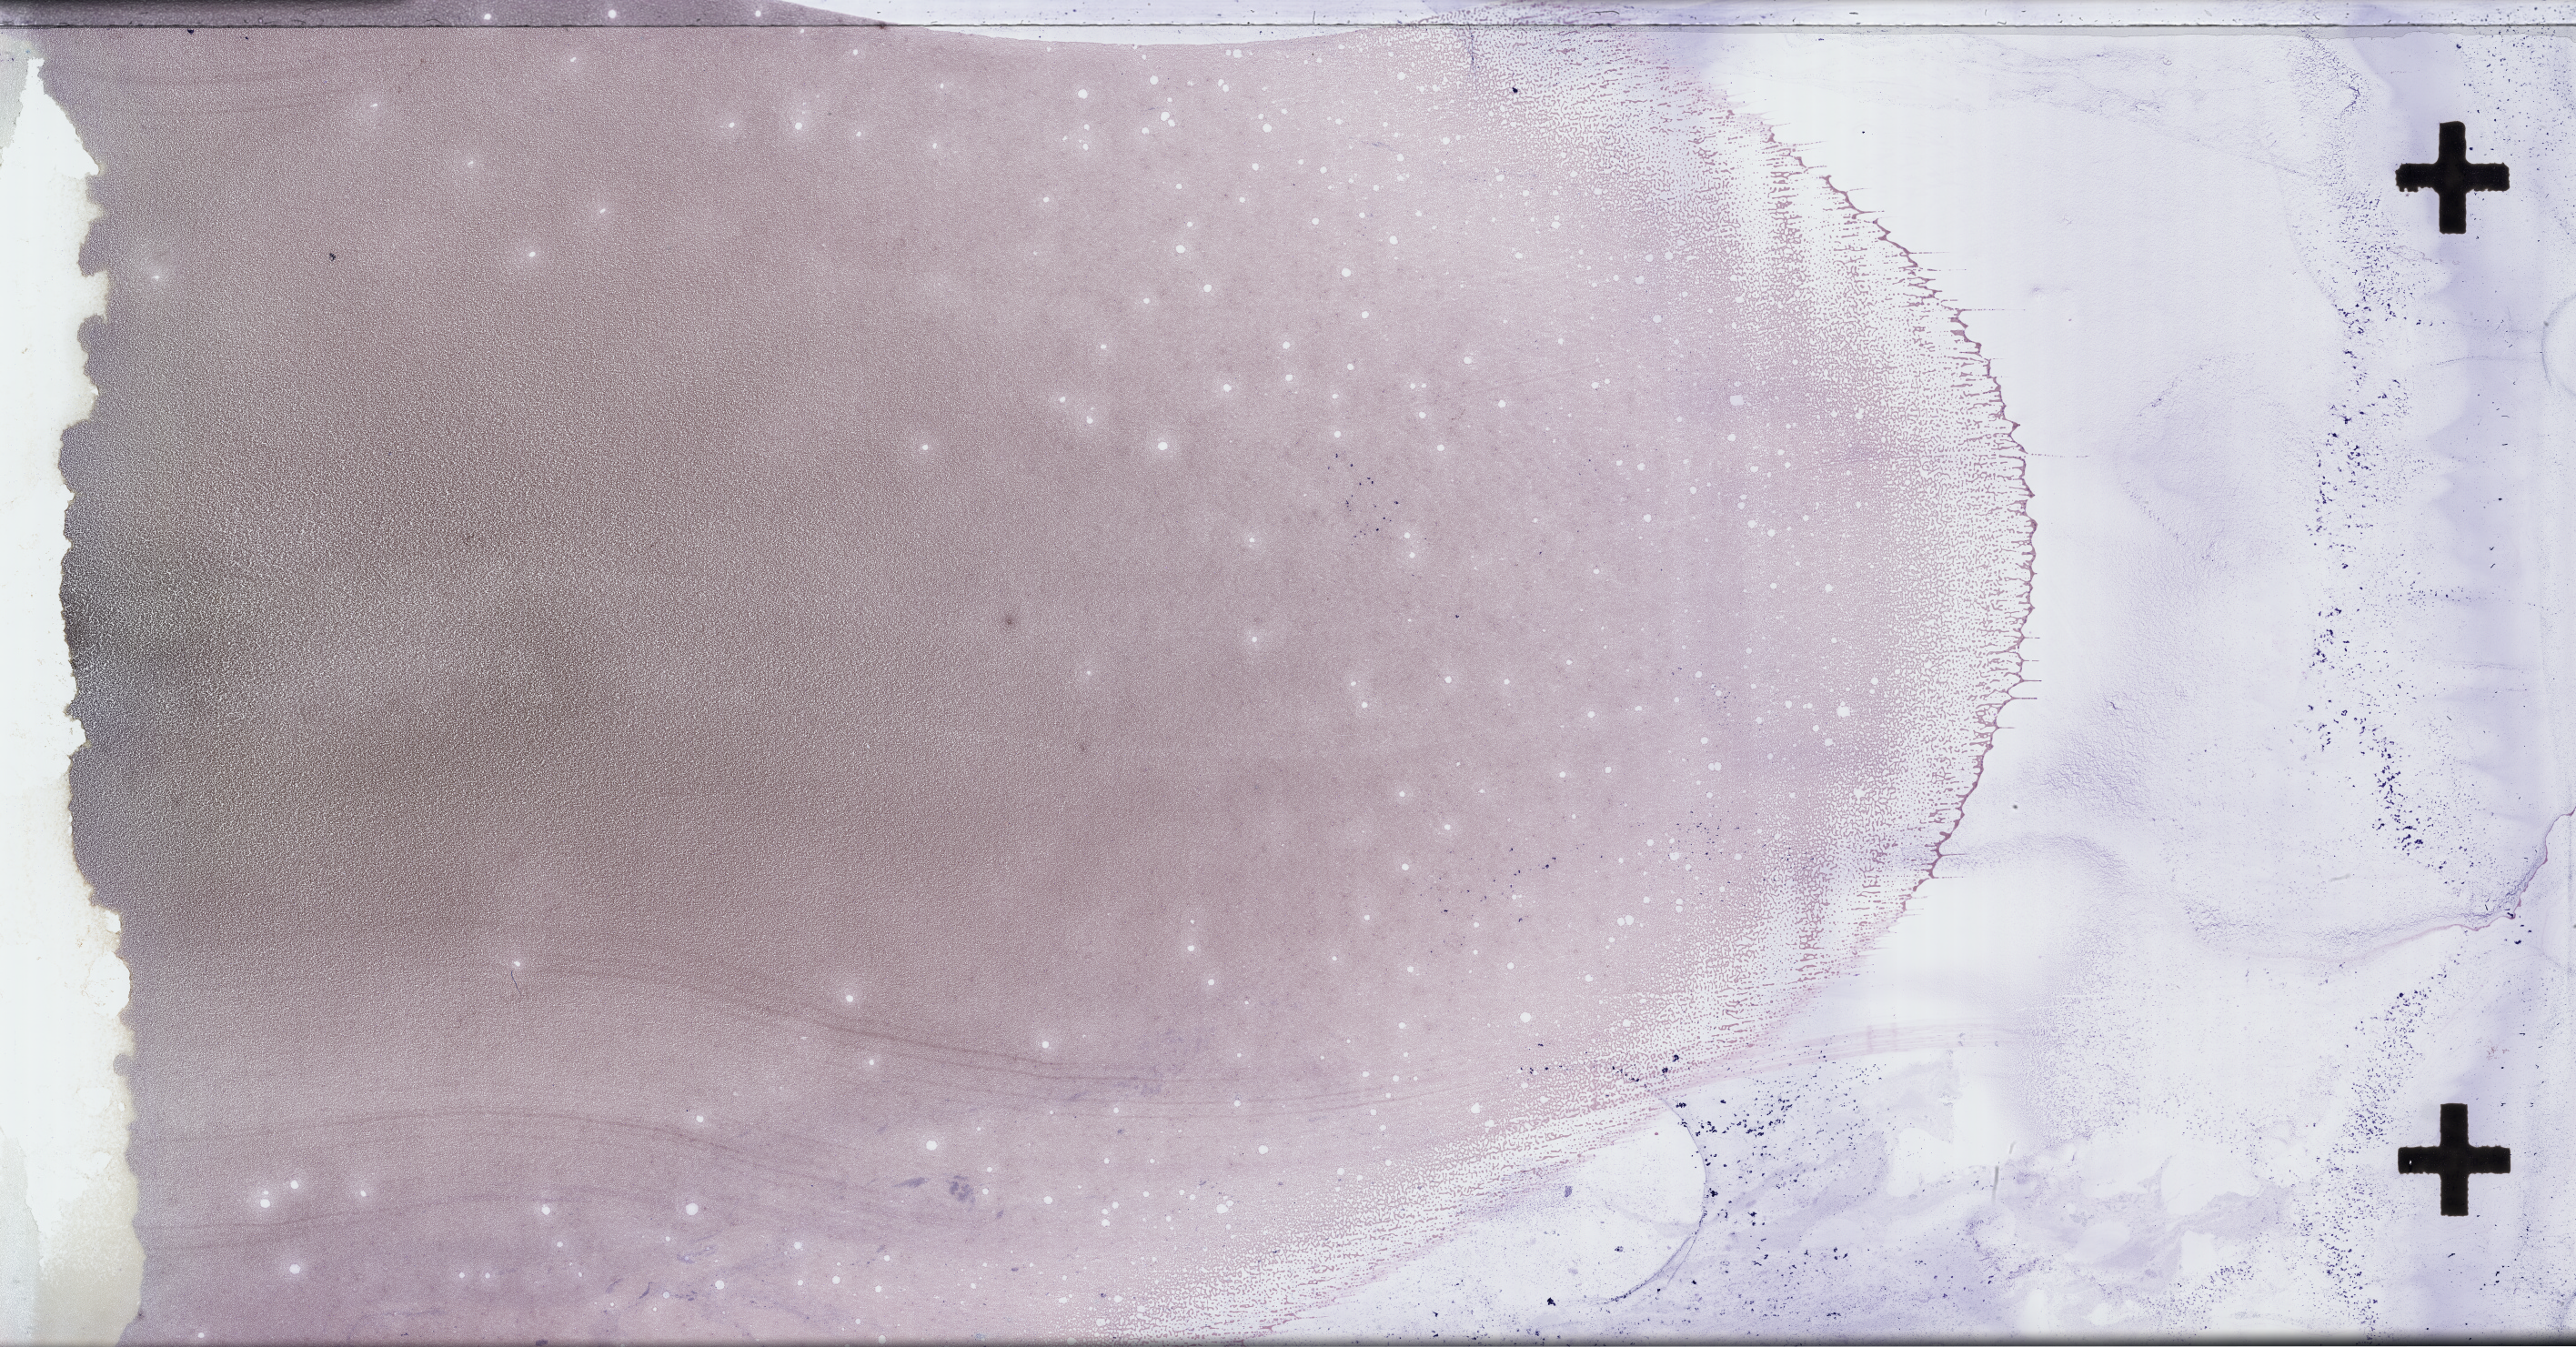
Whole-slide image of a whole blood smear, Wright–Giemsa stain — low-resolution overview of the scanned area, about 45.7 x 23.9 mm; collected at baseline (before treatment). Patient: female.
Patient diagnosis: Plasma Cell Myeloma.